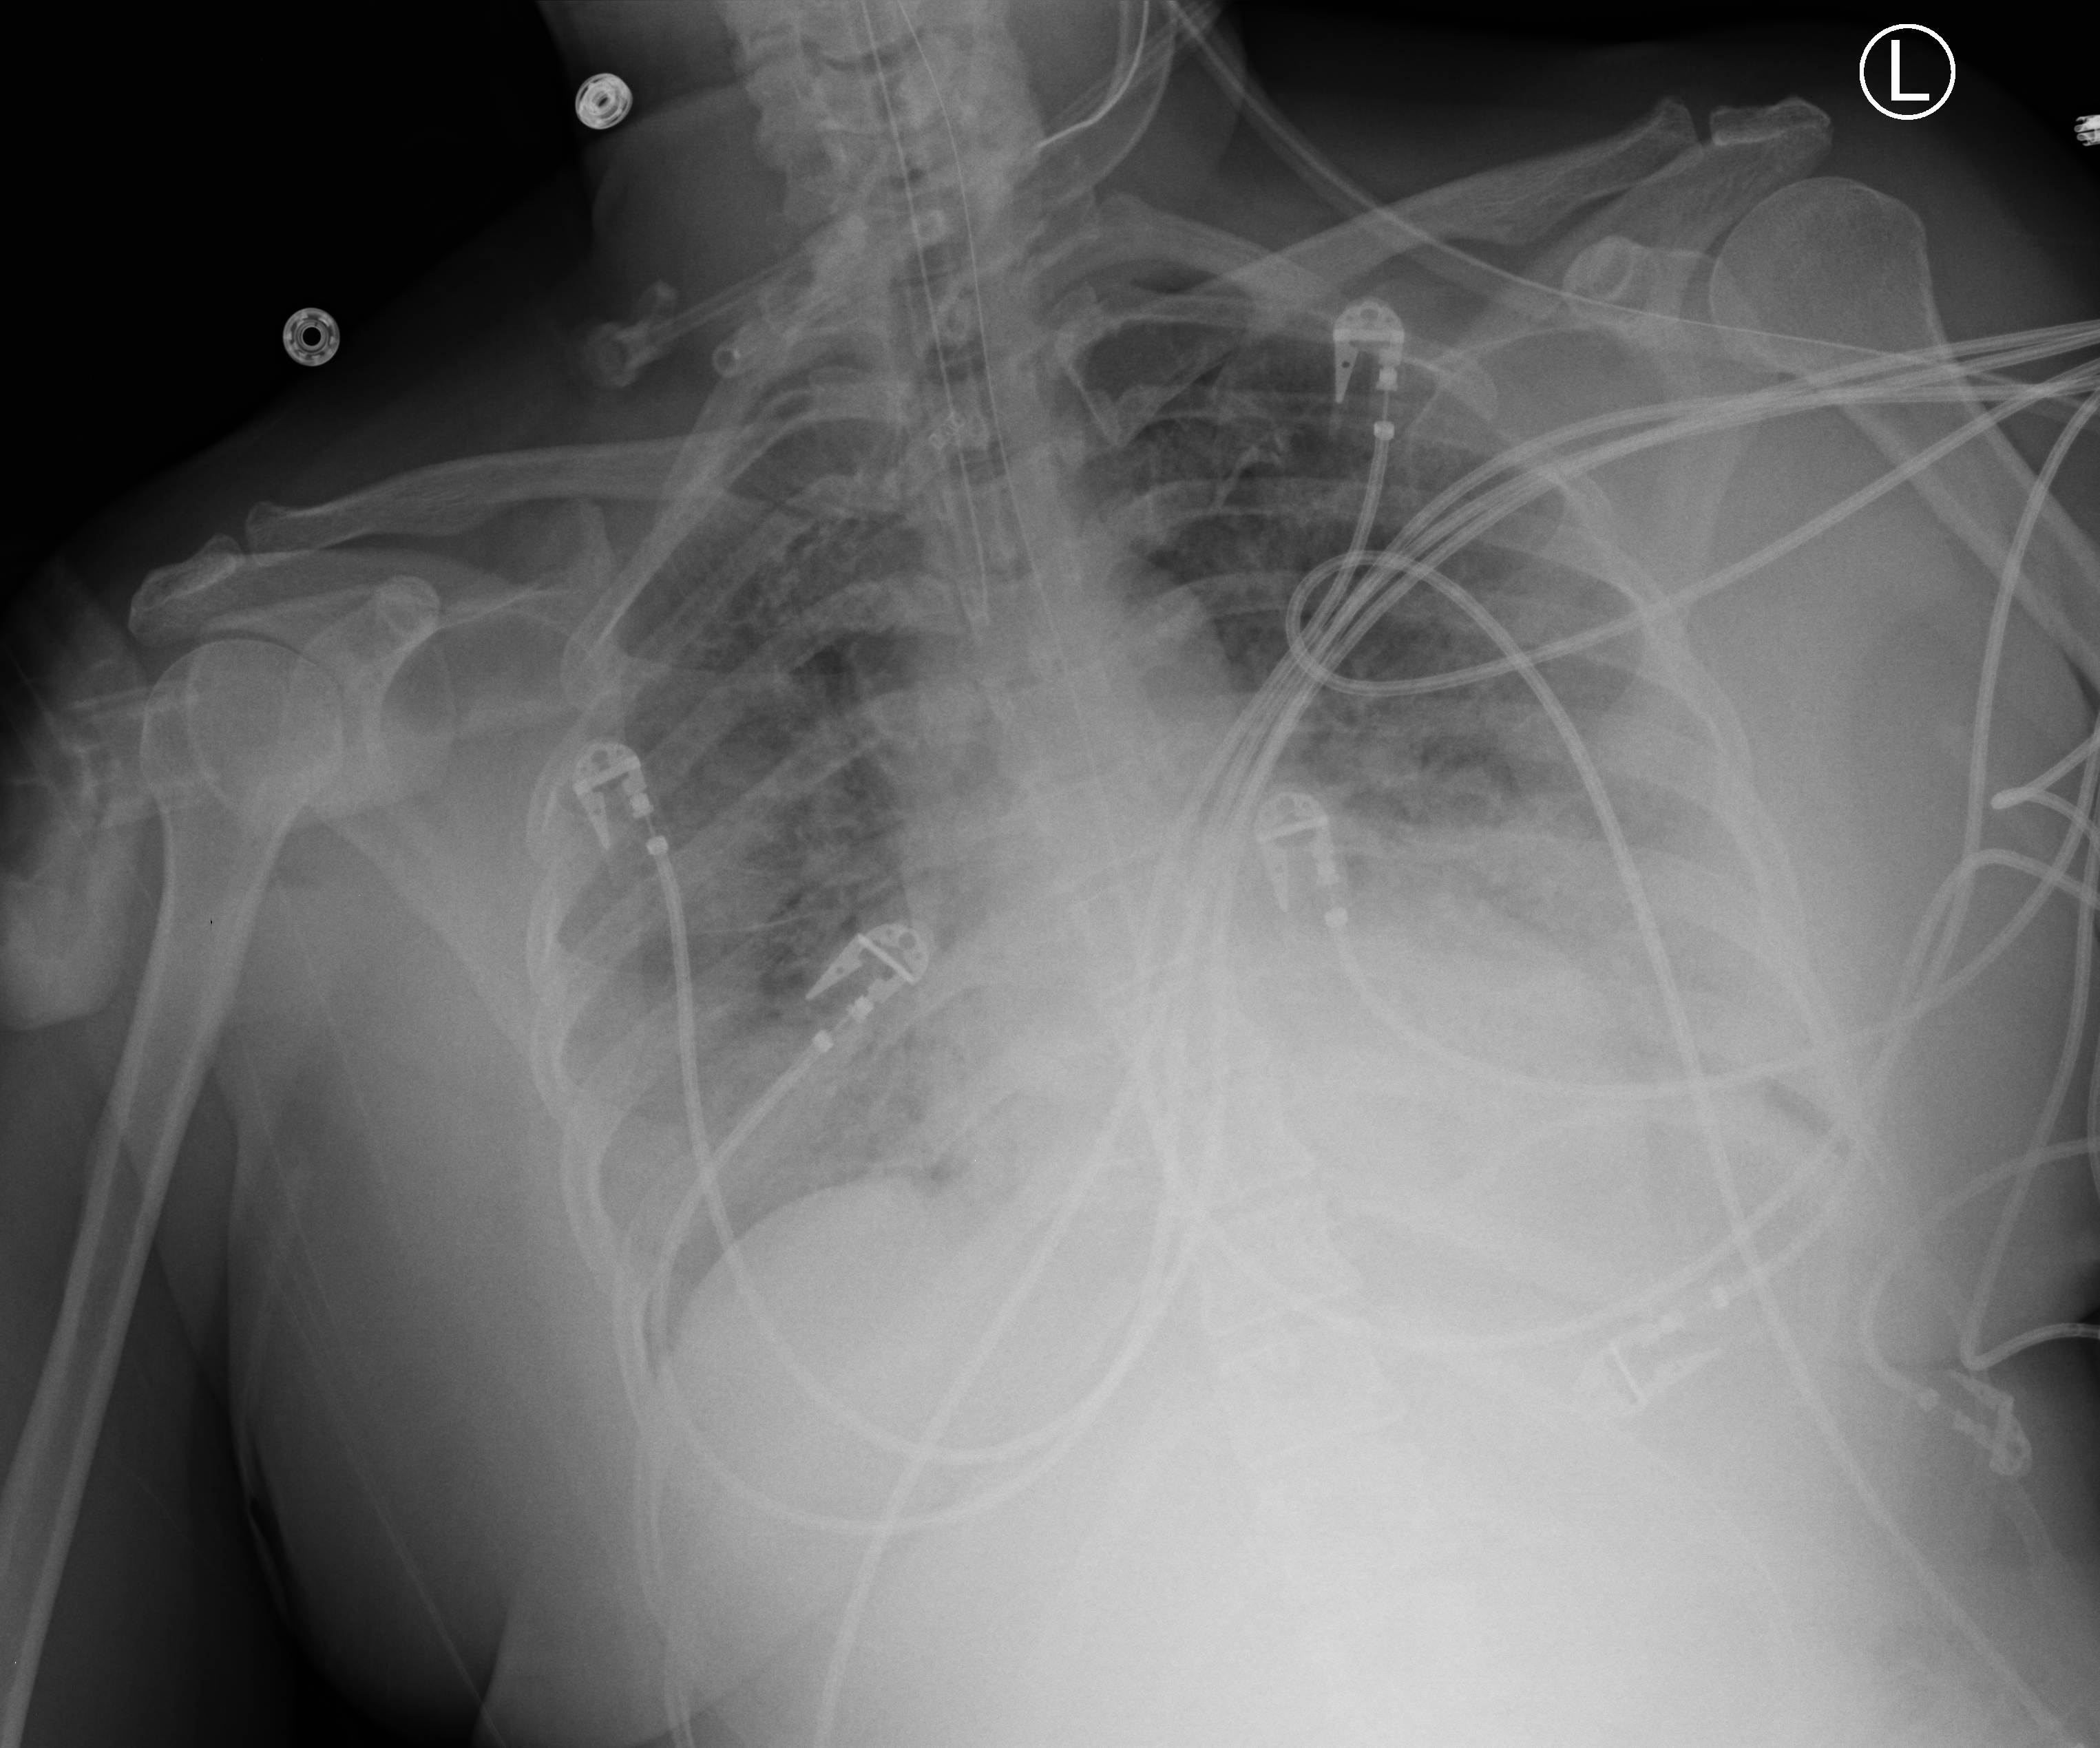
Portable chest radiograph; anteroposterior (AP) projection. Patient hospitalised with COVID-19; male, aged 18–59 years.
Admission-level facts for this patient (not findings on this image; timing relative to this image not recorded): mechanically ventilated during this hospital stay: yes; COPD (admission record): no; admitted to intensive care during this hospital stay: yes.